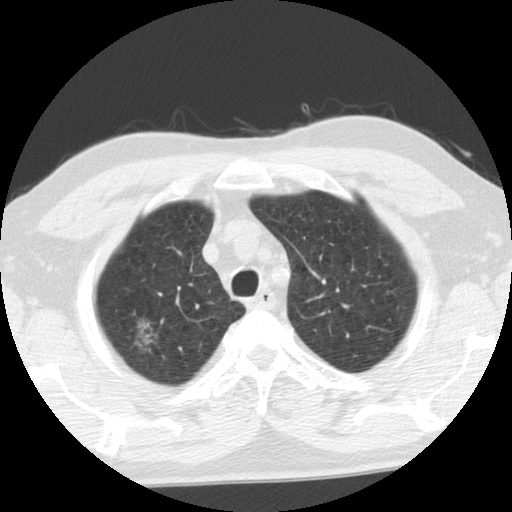
Low-dose screening chest CT, one axial slice. Position 94 of 116 along the scan axis. Reconstruction kernel STANDARD. 140 kVp. Lung window (W 1500 / L -600 HU). 2.5 mm slice thickness. 512 × 512 image matrix.
Outlined on this slice (outlined manually by an expert reader):
- lesion 1 (tumor, upper lobe of right lung): box from (x=133, y=319) to (x=157, y=352) px